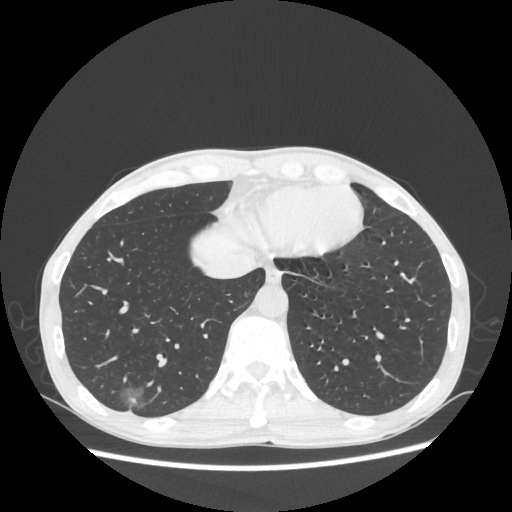
Chest CT, one axial slice; reconstruction kernel STANDARD; lung window (W 1500 / L -600 HU); 1.25 mm slice thickness; 512 × 512 image matrix, field of view 360 × 360 mm. Patient: male, 60 years. From the clinical record (not read from this slice): clinical TNM (as recorded): T1c N0 M0.
Outlined on this slice (rectangle marked by the reading radiologist):
- lung tumour (recorded histology: adenocarcinoma): bounding box [x1, y1, x2, y2] px = [116, 378, 158, 421]